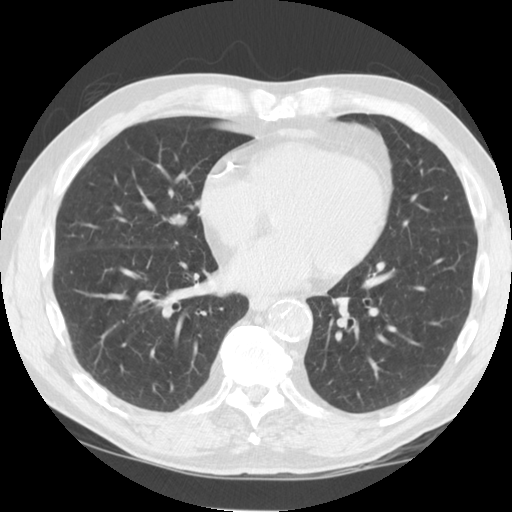
Low-dose screening chest CT, one axial slice; position 46 of 125 along the scan axis; reconstruction kernel STANDARD; 120 kVp; lung window (W 1500 / L -600 HU); 512 × 512 image matrix.
Annotated regions visible in this slice (manually delineated by an expert):
- lesion 1 (tumor, middle lobe of right lung): bounding box [x1, y1, x2, y2] px = [168, 213, 187, 224]